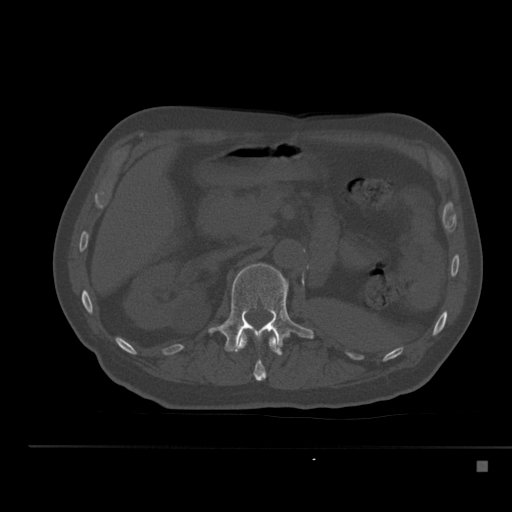
CT including the spine, one axial slice; position 211 of 517 along the scan axis; reconstruction kernel Br40s; 120 kVp; bone window (W 1800 / L 400 HU); 1.5 mm slice thickness; 512 × 512 image matrix. Patient: male, 70 years. From the clinical record (not read from this slice): primary cancer: renal.
Outlined on this slice (semi-automatically segmented with operator editing):
- L1 vertebra: bounding box [x1, y1, x2, y2] px = [208, 263, 314, 352]
- T12 vertebra: [233, 333, 282, 381]